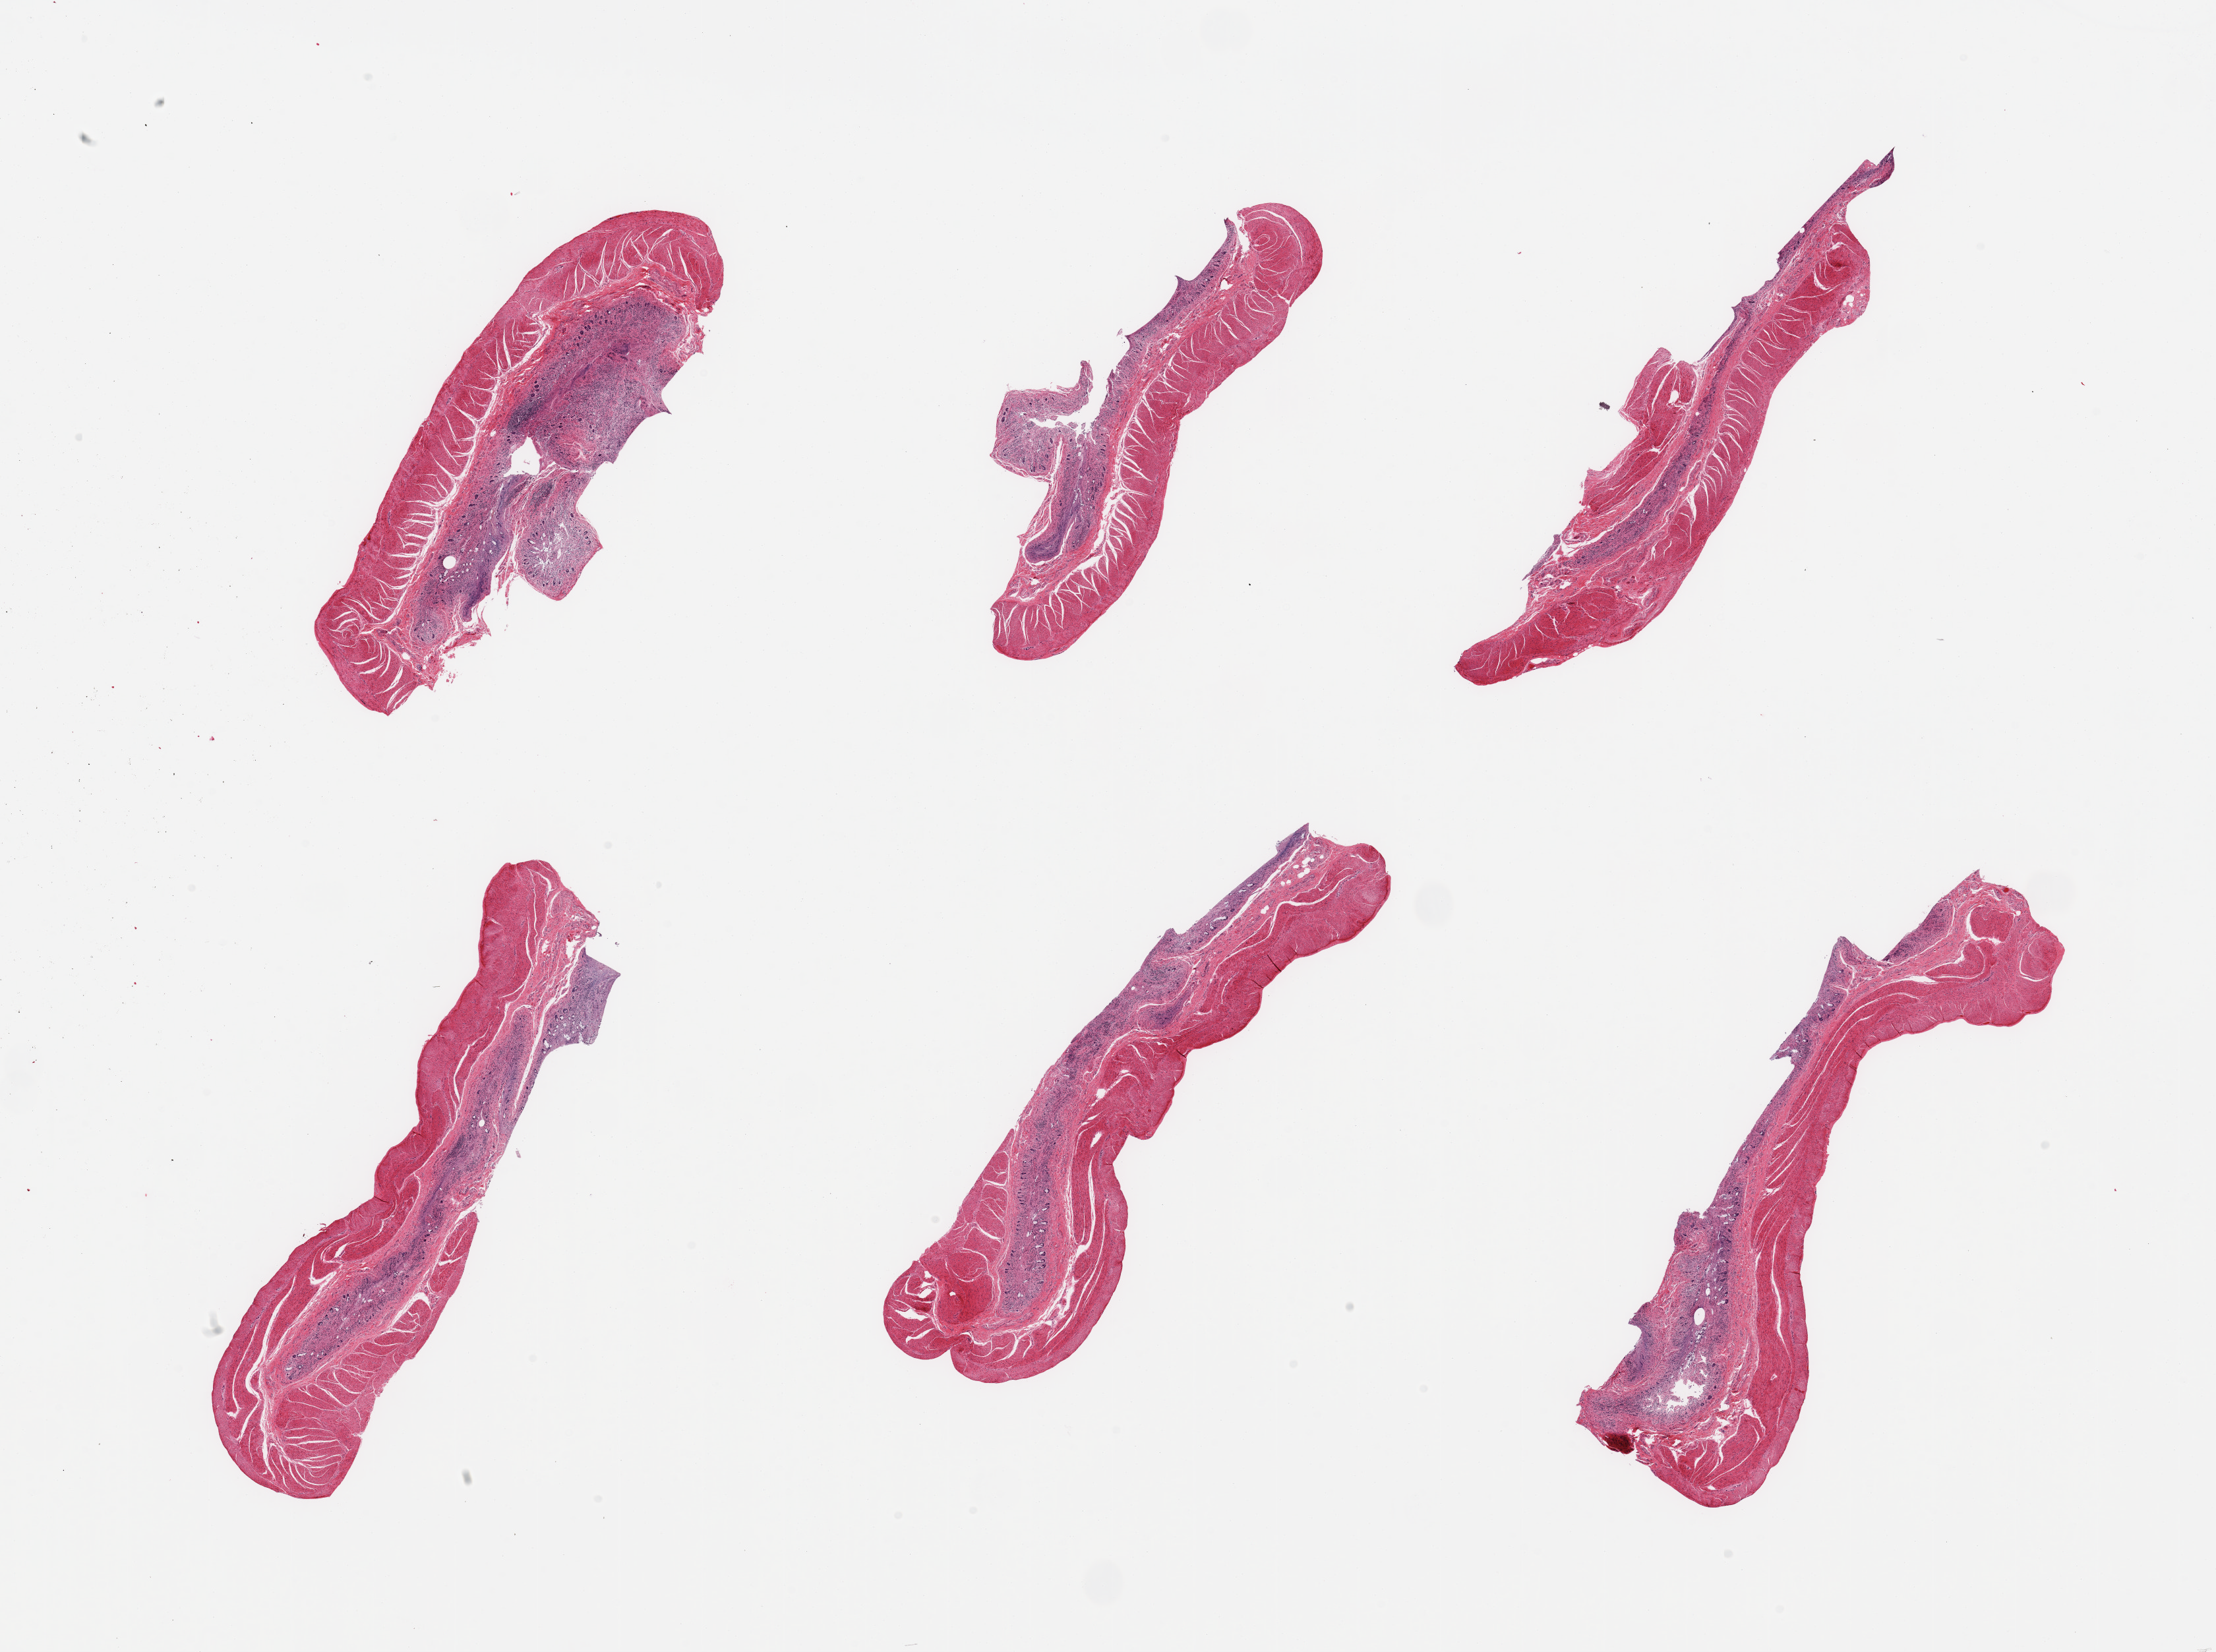
H&E whole-slide image — low-resolution overview of the scanned area, about 26.6 x 19.8 mm, PAXgene-fixed, paraffin-embedded tissue, target tissue: ileum, tissue donor sample. Male donor.
Reviewer comment on this tissue sample: 6 pieces, autolyzed mucosa; minimal target lymphoid aggregates.